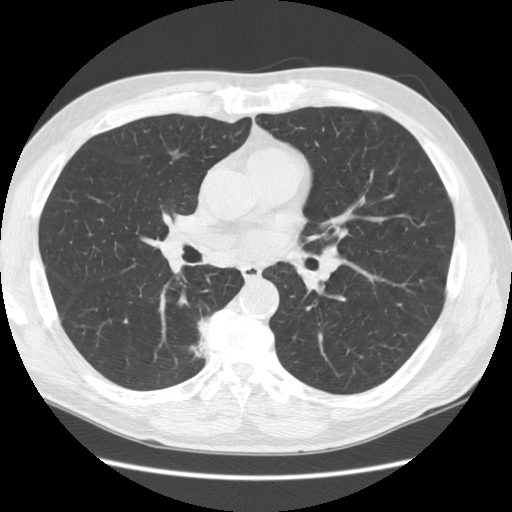
Low-dose screening chest CT, one axial slice. Slice 70 of 133 in the series (ordered by position). Reconstruction kernel STANDARD. 120 kVp. Lung window (W 1500 / L -600 HU). 2.5 mm slice thickness. 512 × 512 image matrix, field of view 370 × 370 mm.
Structures marked on this image (outlined manually by an expert reader):
- lesion 1 (tumor, lower lobe of right lung): box from (x=191, y=317) to (x=210, y=360) px